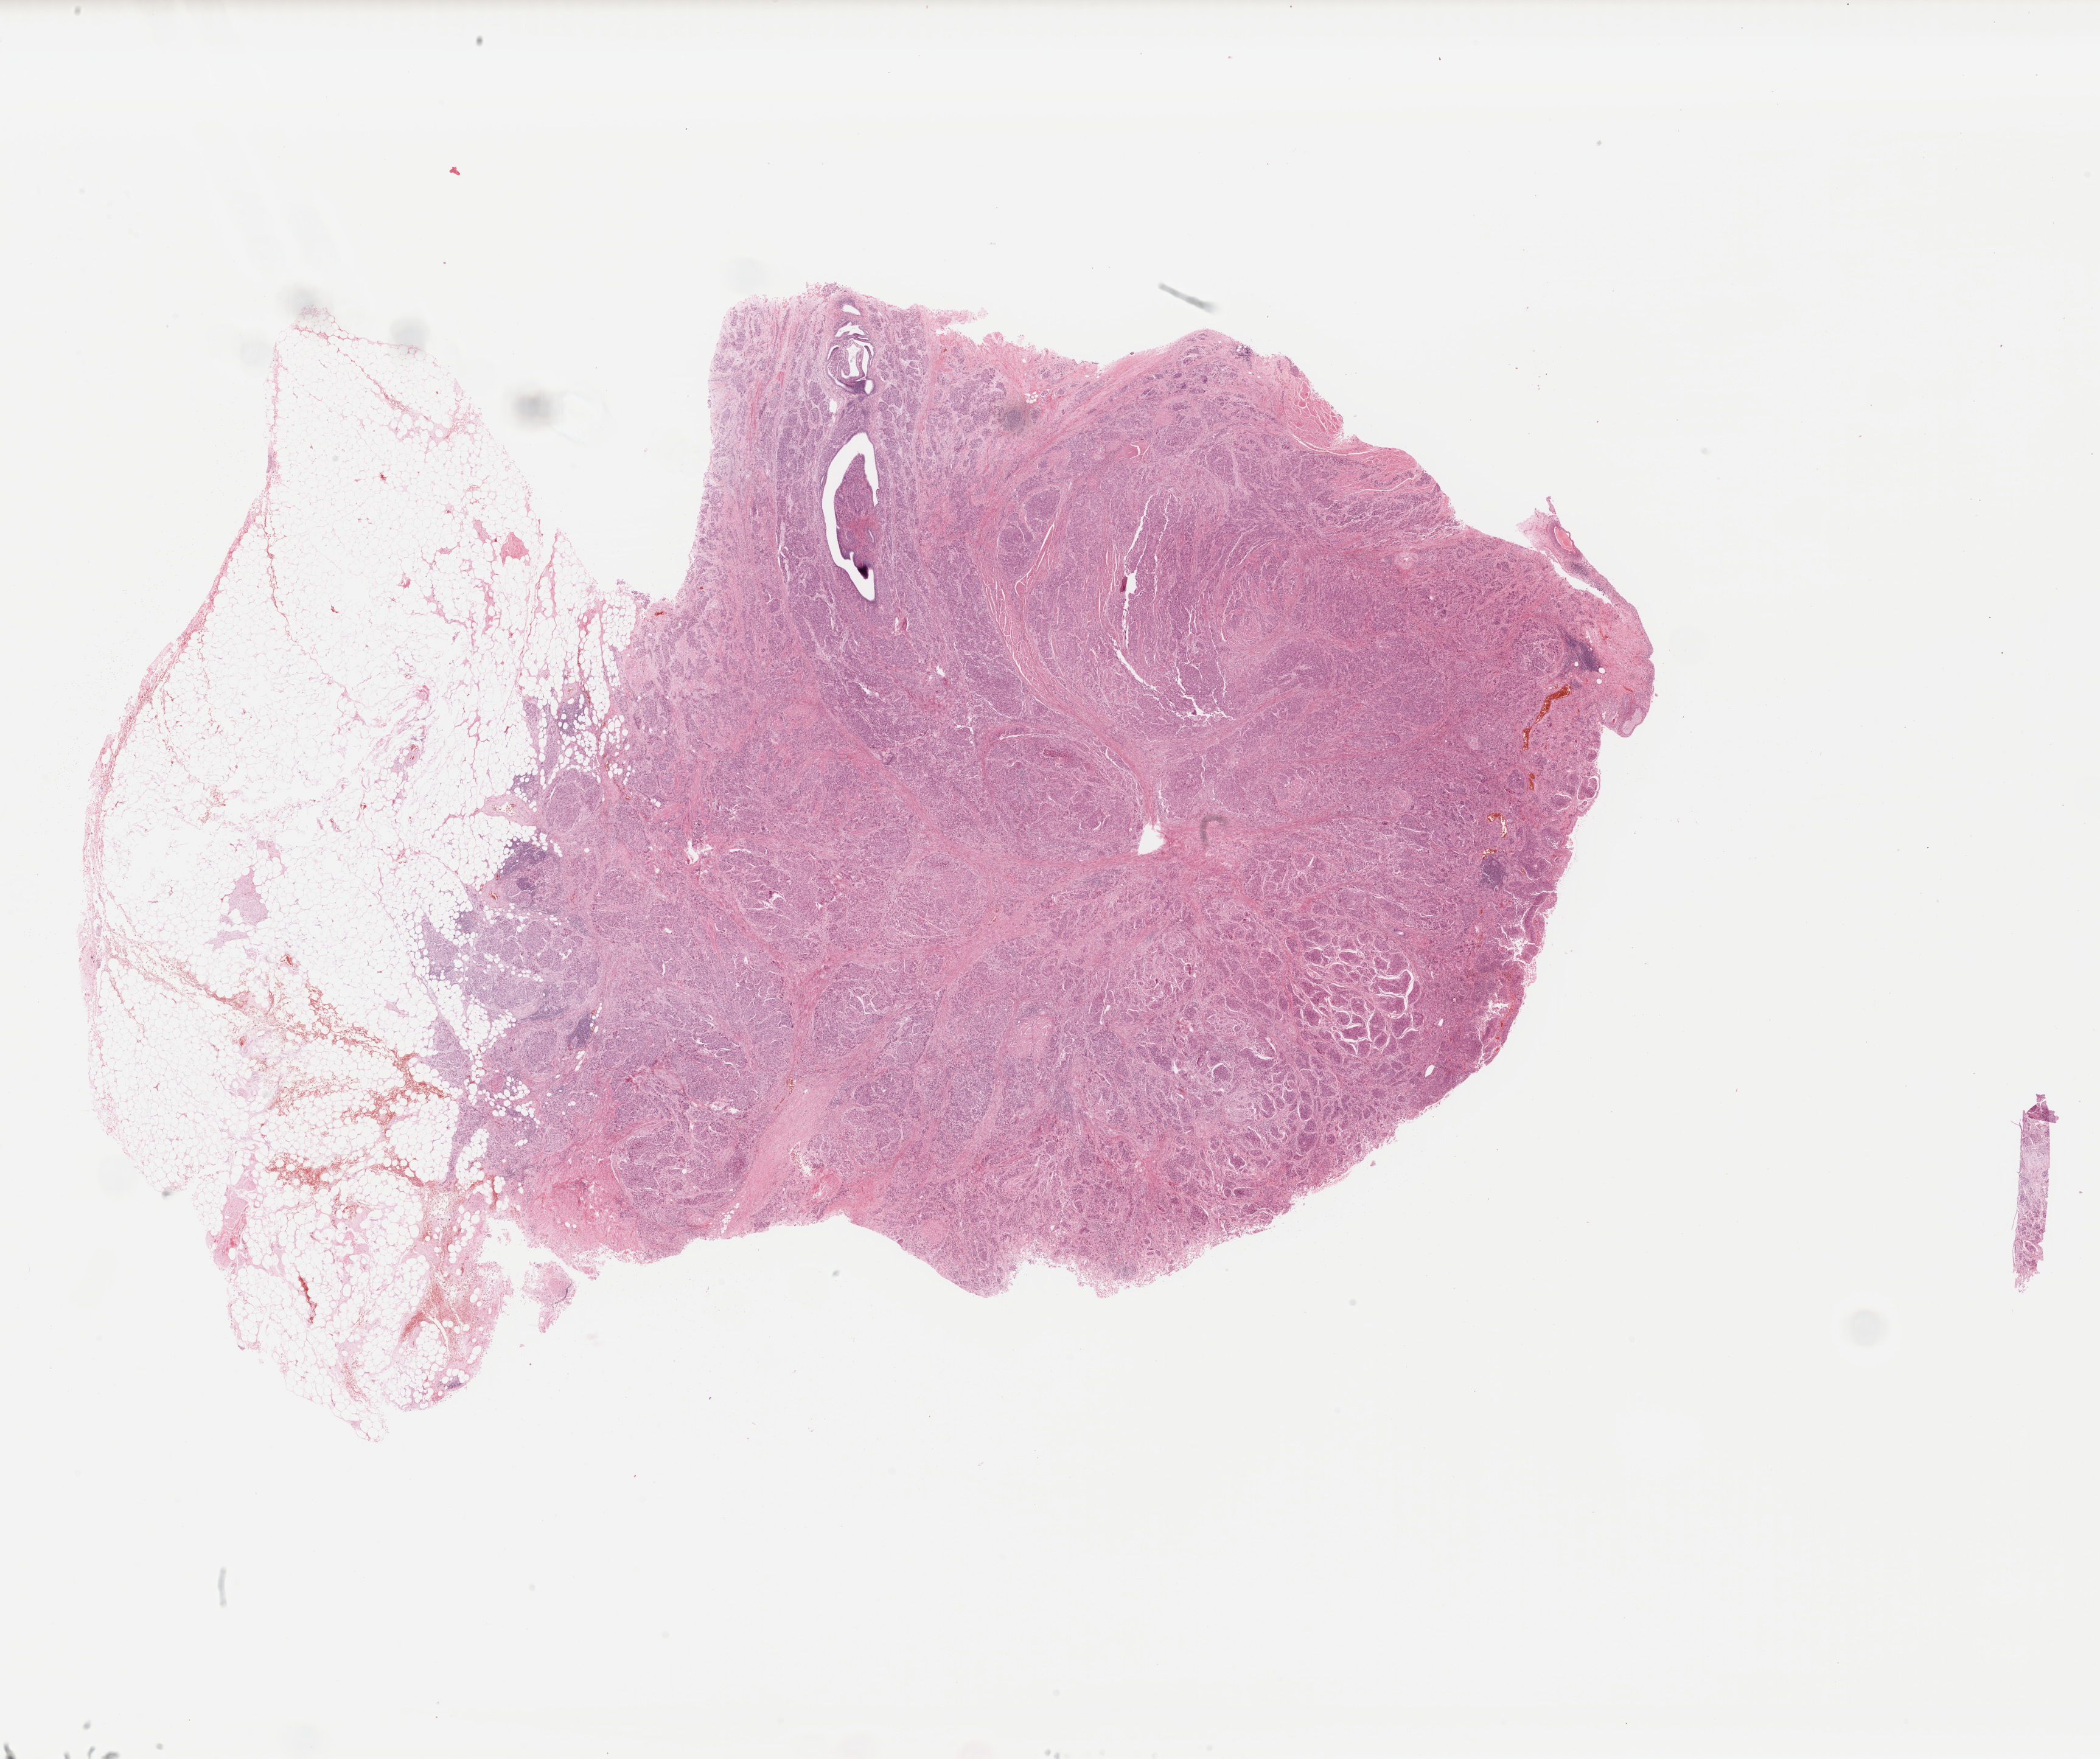
Whole-slide histology image, H&E — whole scanned area (about 27.2 x 22.8 mm) shown as a low-resolution overview, formalin-fixed paraffin-embedded (FFPE) diagnostic section, sample: primary tumour, bladder. Male, age 66 years at initial diagnosis. Histologic grade: high grade.
AJCC pathologic stage: IV (7th edition). Diagnosis: Transitional cell carcinoma.